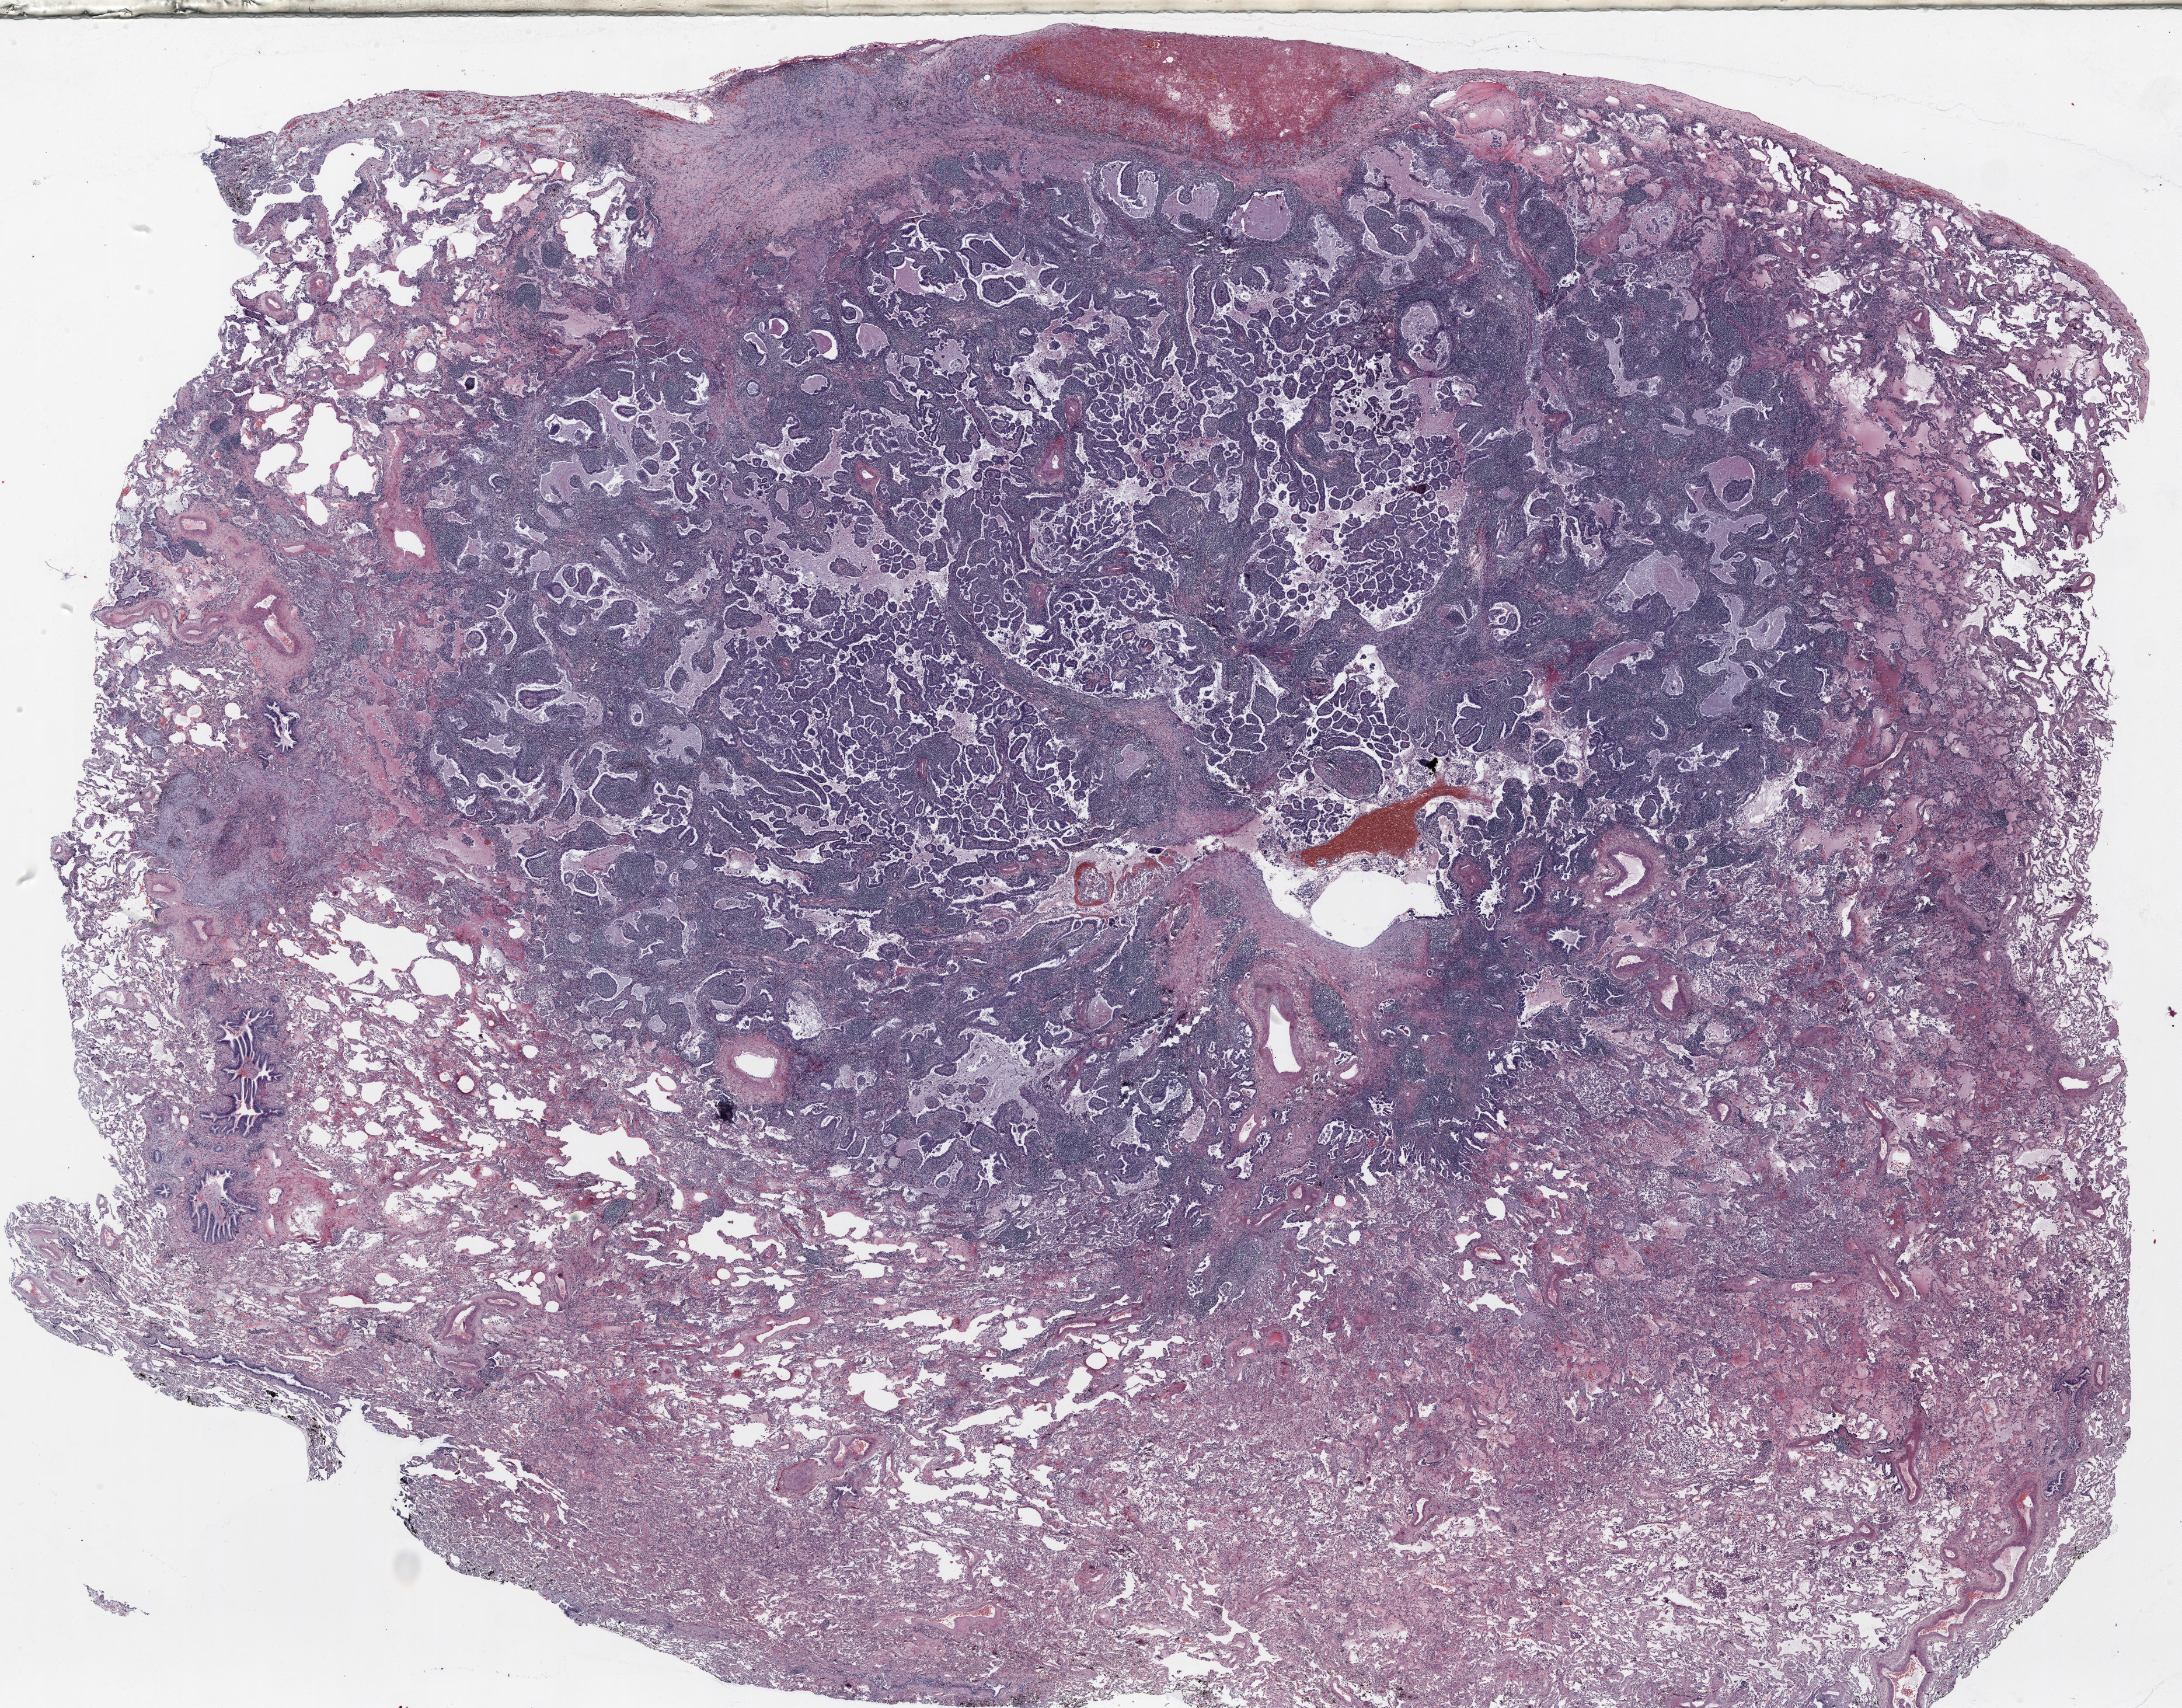
H&E whole-slide image, whole scanned area (about 30.0 x 23.5 mm) shown as a low-resolution overview; FFPE section; lung. Male patient, aged 71 at enrolment. Former smoker at enrolment. Grade: poorly differentiated (G3).
- tumour size (pathology): 28 mm
- participant's lung-cancer diagnosis: Adenocarcinoma, NOS (ICD-O-3 8140/3)
- ICD-O-3 topography: lower lobe of lung (C34.3)
- stage (AJCC 6th edition): IA
- primary tumour location (clinical record): left lower lobe